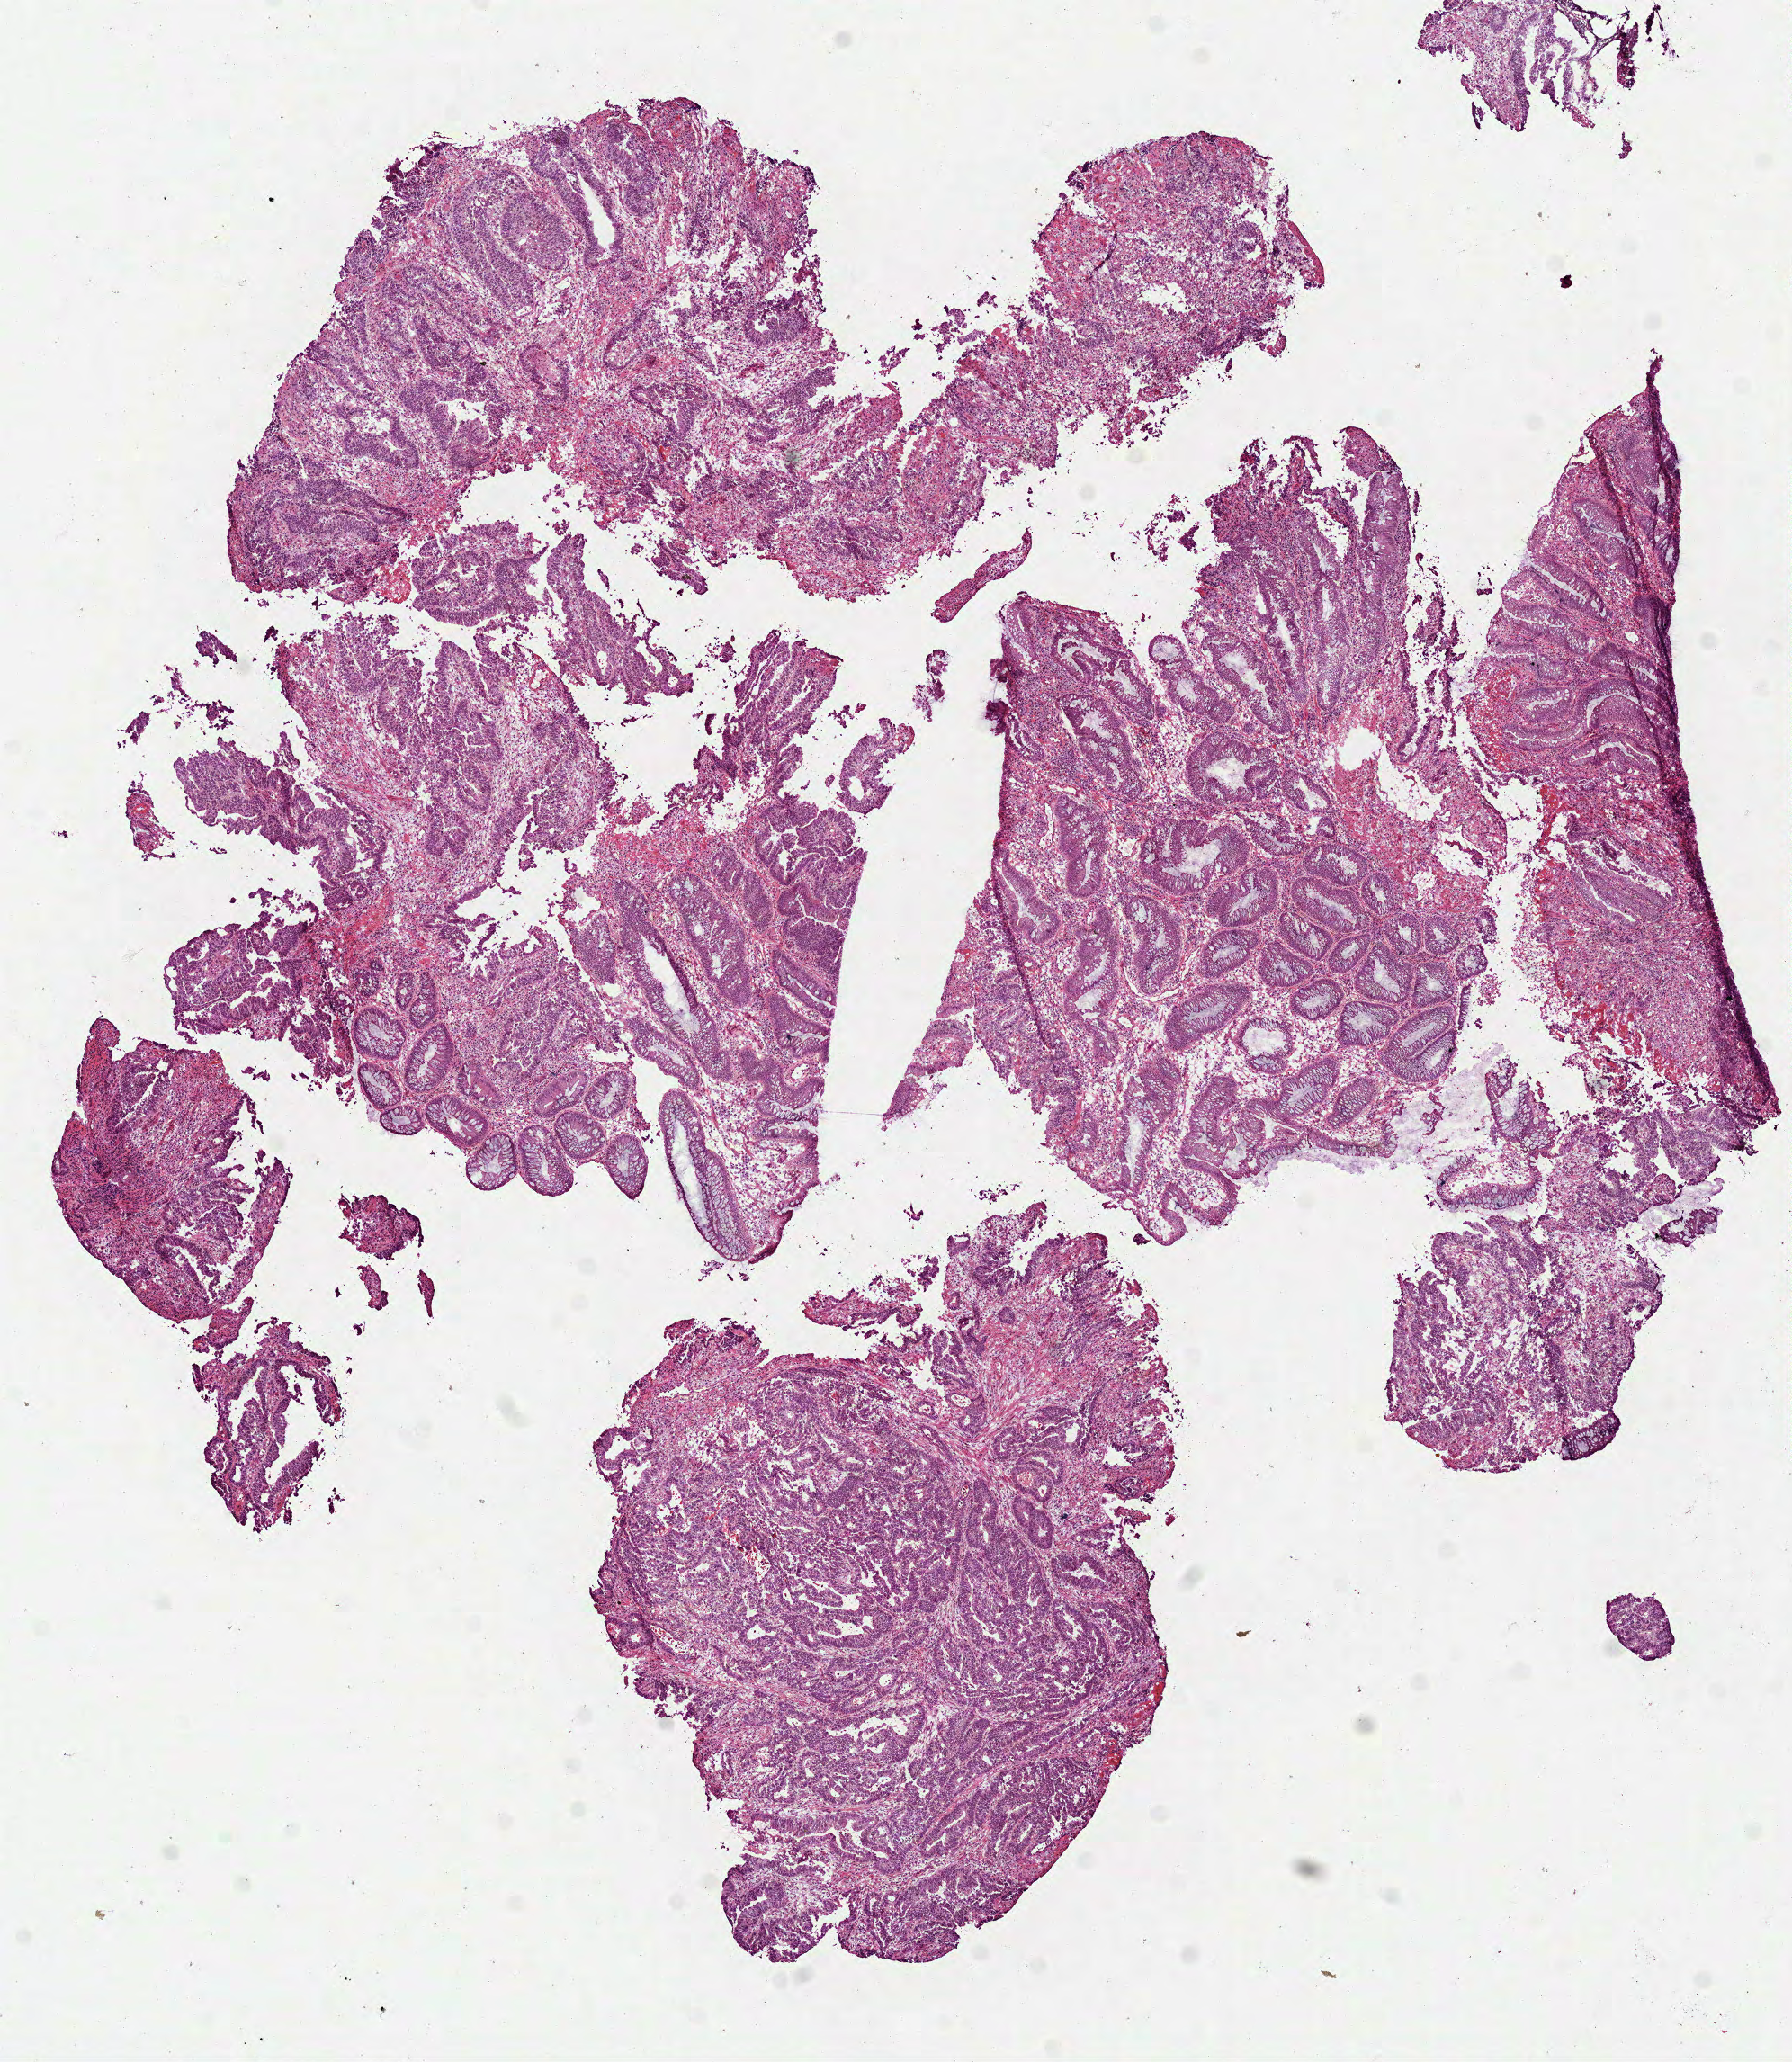
Digitized Hematoxylin and eosin (H&E) stained tissue section (whole slide), whole scanned area (about 8.0 x 9.2 mm, acquisition: 40x scan) shown as a low-resolution overview. Frozen section from the bottom of the tissue portion. Sample: primary tumour, rectum. Male patient; age at initial diagnosis 63 years. Slide review estimates, as recorded: tumour cells 50%, tumour nuclei 50%, normal cells 30%, stromal cells 15%, necrosis 5%.
AJCC pathologic stage: IIIB. Diagnosis: Adenocarcinoma, NOS. Lymph nodes positive (case pathology): 0 of 2 examined.